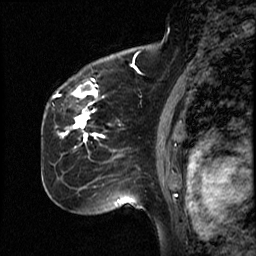
Breast MRI (dynamic contrast-enhanced), one sagittal slice; position 35 of 50 along the scan axis; dynamic contrast-enhanced study with each time point stored as its own series, time point 2 of 4 at this slice position (early post-contrast, ordered by acquisition time); 1.5 T; TE 4.2 ms, TR 18.5 ms; 256 × 256 image matrix, field of view 200 × 200 mm. Patient: female, 44 years. Case-level facts recorded for this patient, not image findings: setting: breast cancer imaged before/during neoadjuvant chemotherapy; receptor status: HR-positive, HER2-negative.
Structures marked on this image (semi-automatically segmented with operator editing):
- analysis volume of interest (the breast-tissue region the enhancement analysis was run in; not a lesion): bounding box [x1, y1, x2, y2] px = [59, 80, 114, 206]
- tumour enhancement mask (voxels above the 100 % enhancement threshold inside the analysis volume of interest): [62, 109, 103, 143]